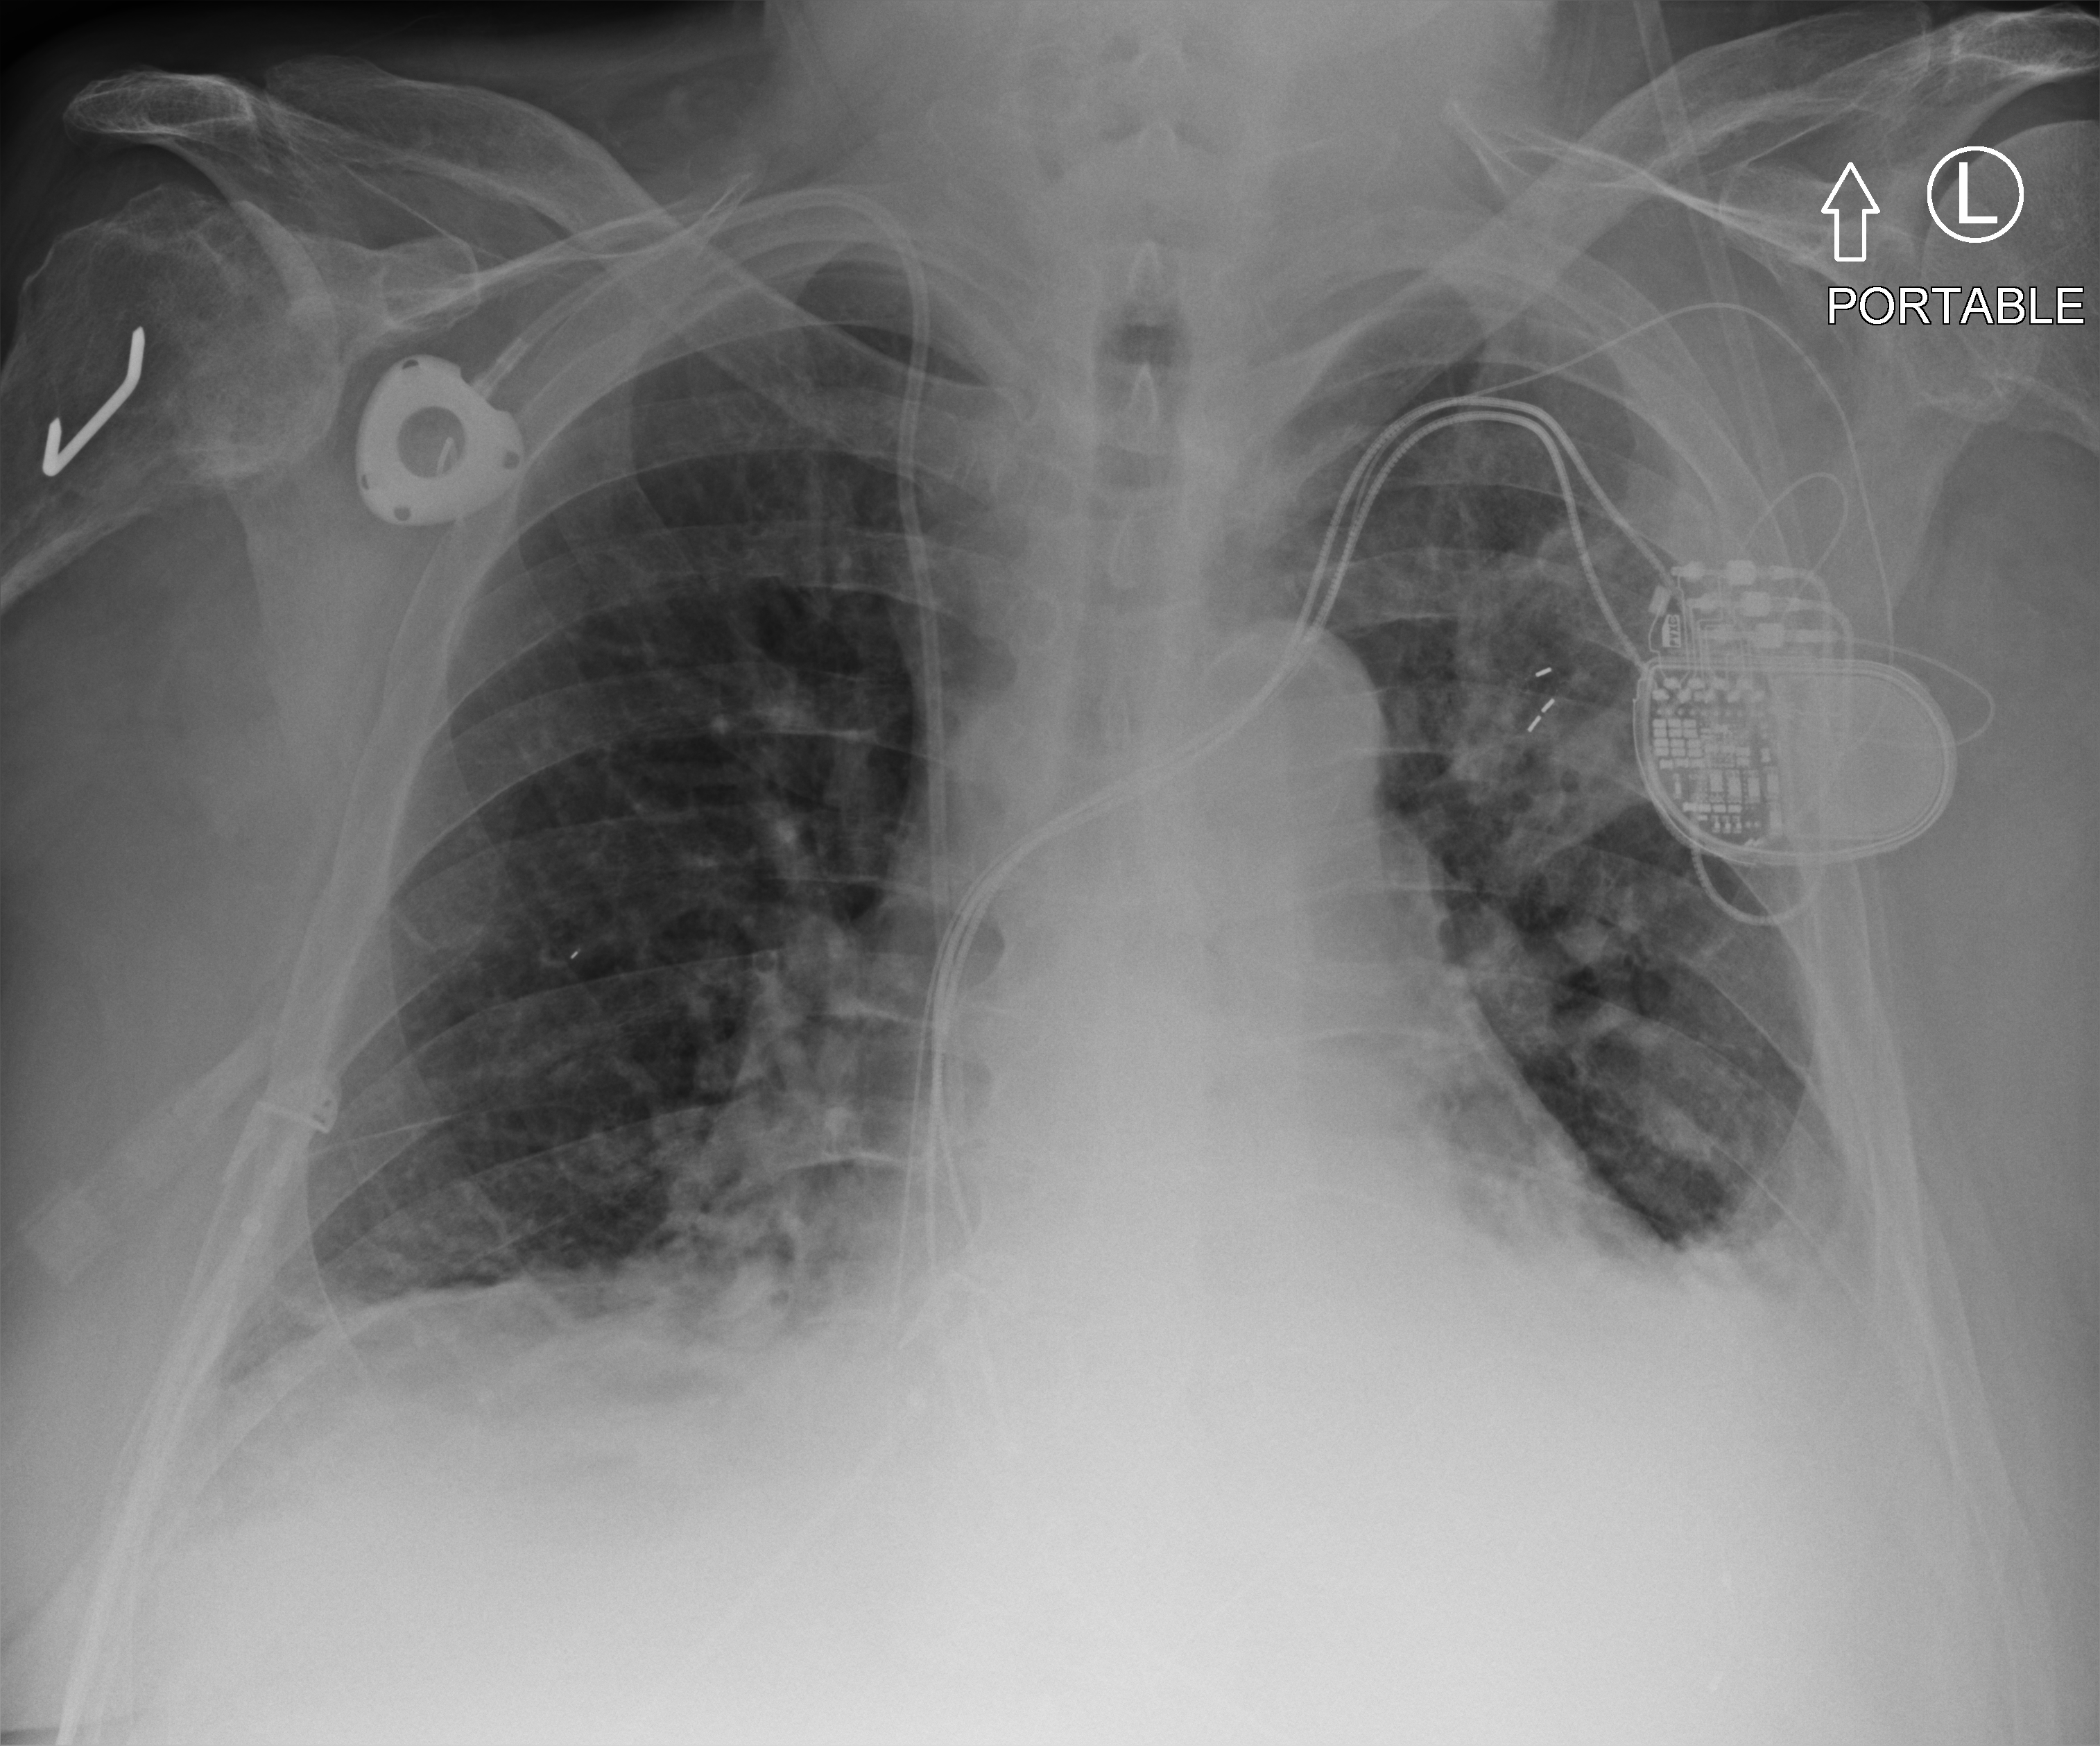
Bedside chest radiograph (computed radiography). Patient hospitalised with COVID-19; male, aged 60–74 years.
From the hospital-stay record, not from the radiograph (when in the stay this image was taken is not recorded): mechanically ventilated during this hospital stay: no.